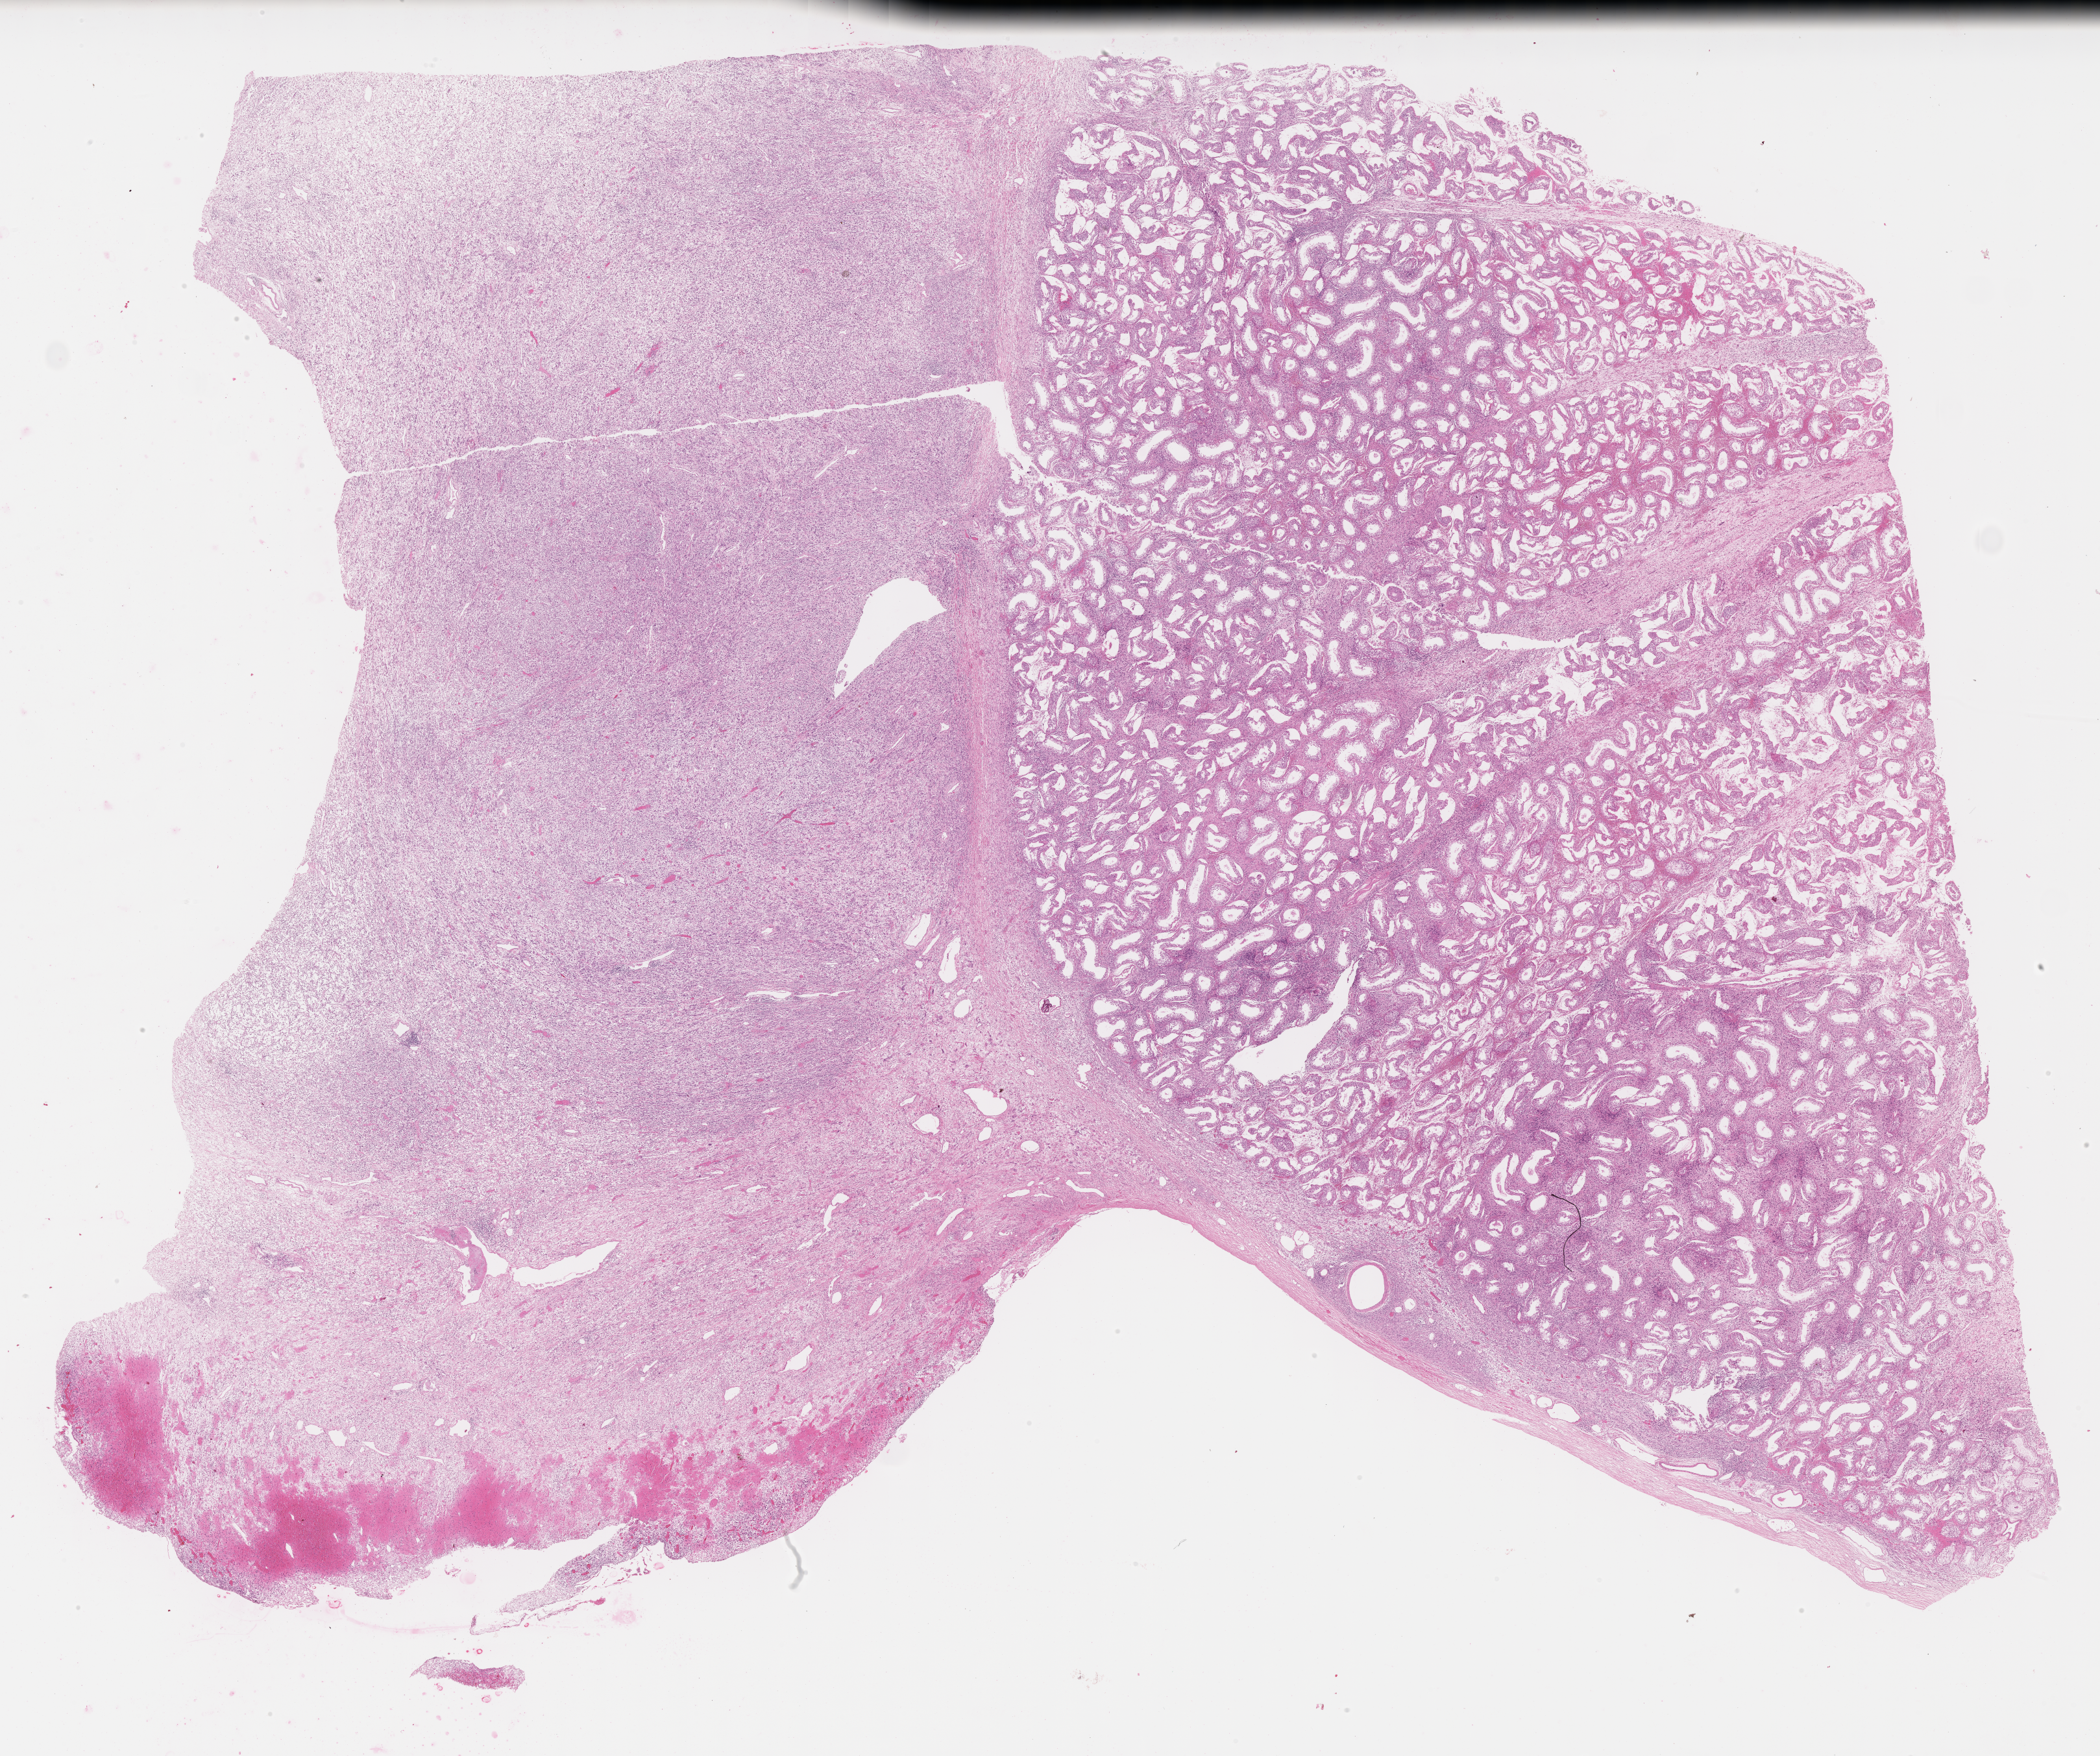
Digitized hematoxylin and eosin (H&E)-stained section of tumor tissue, a low-resolution overview of the entire scanned area, about 26.2 x 21.9 mm. FFPE section. Site: paratesticular, right. Male patient, age at diagnosis 15.1 years.
Metastatic status at presentation (as recorded): non-metastatic (unconfirmed). Diagnosis: rhabdomyosarcoma; histological classification: embryonal rhabdomyosarcoma.